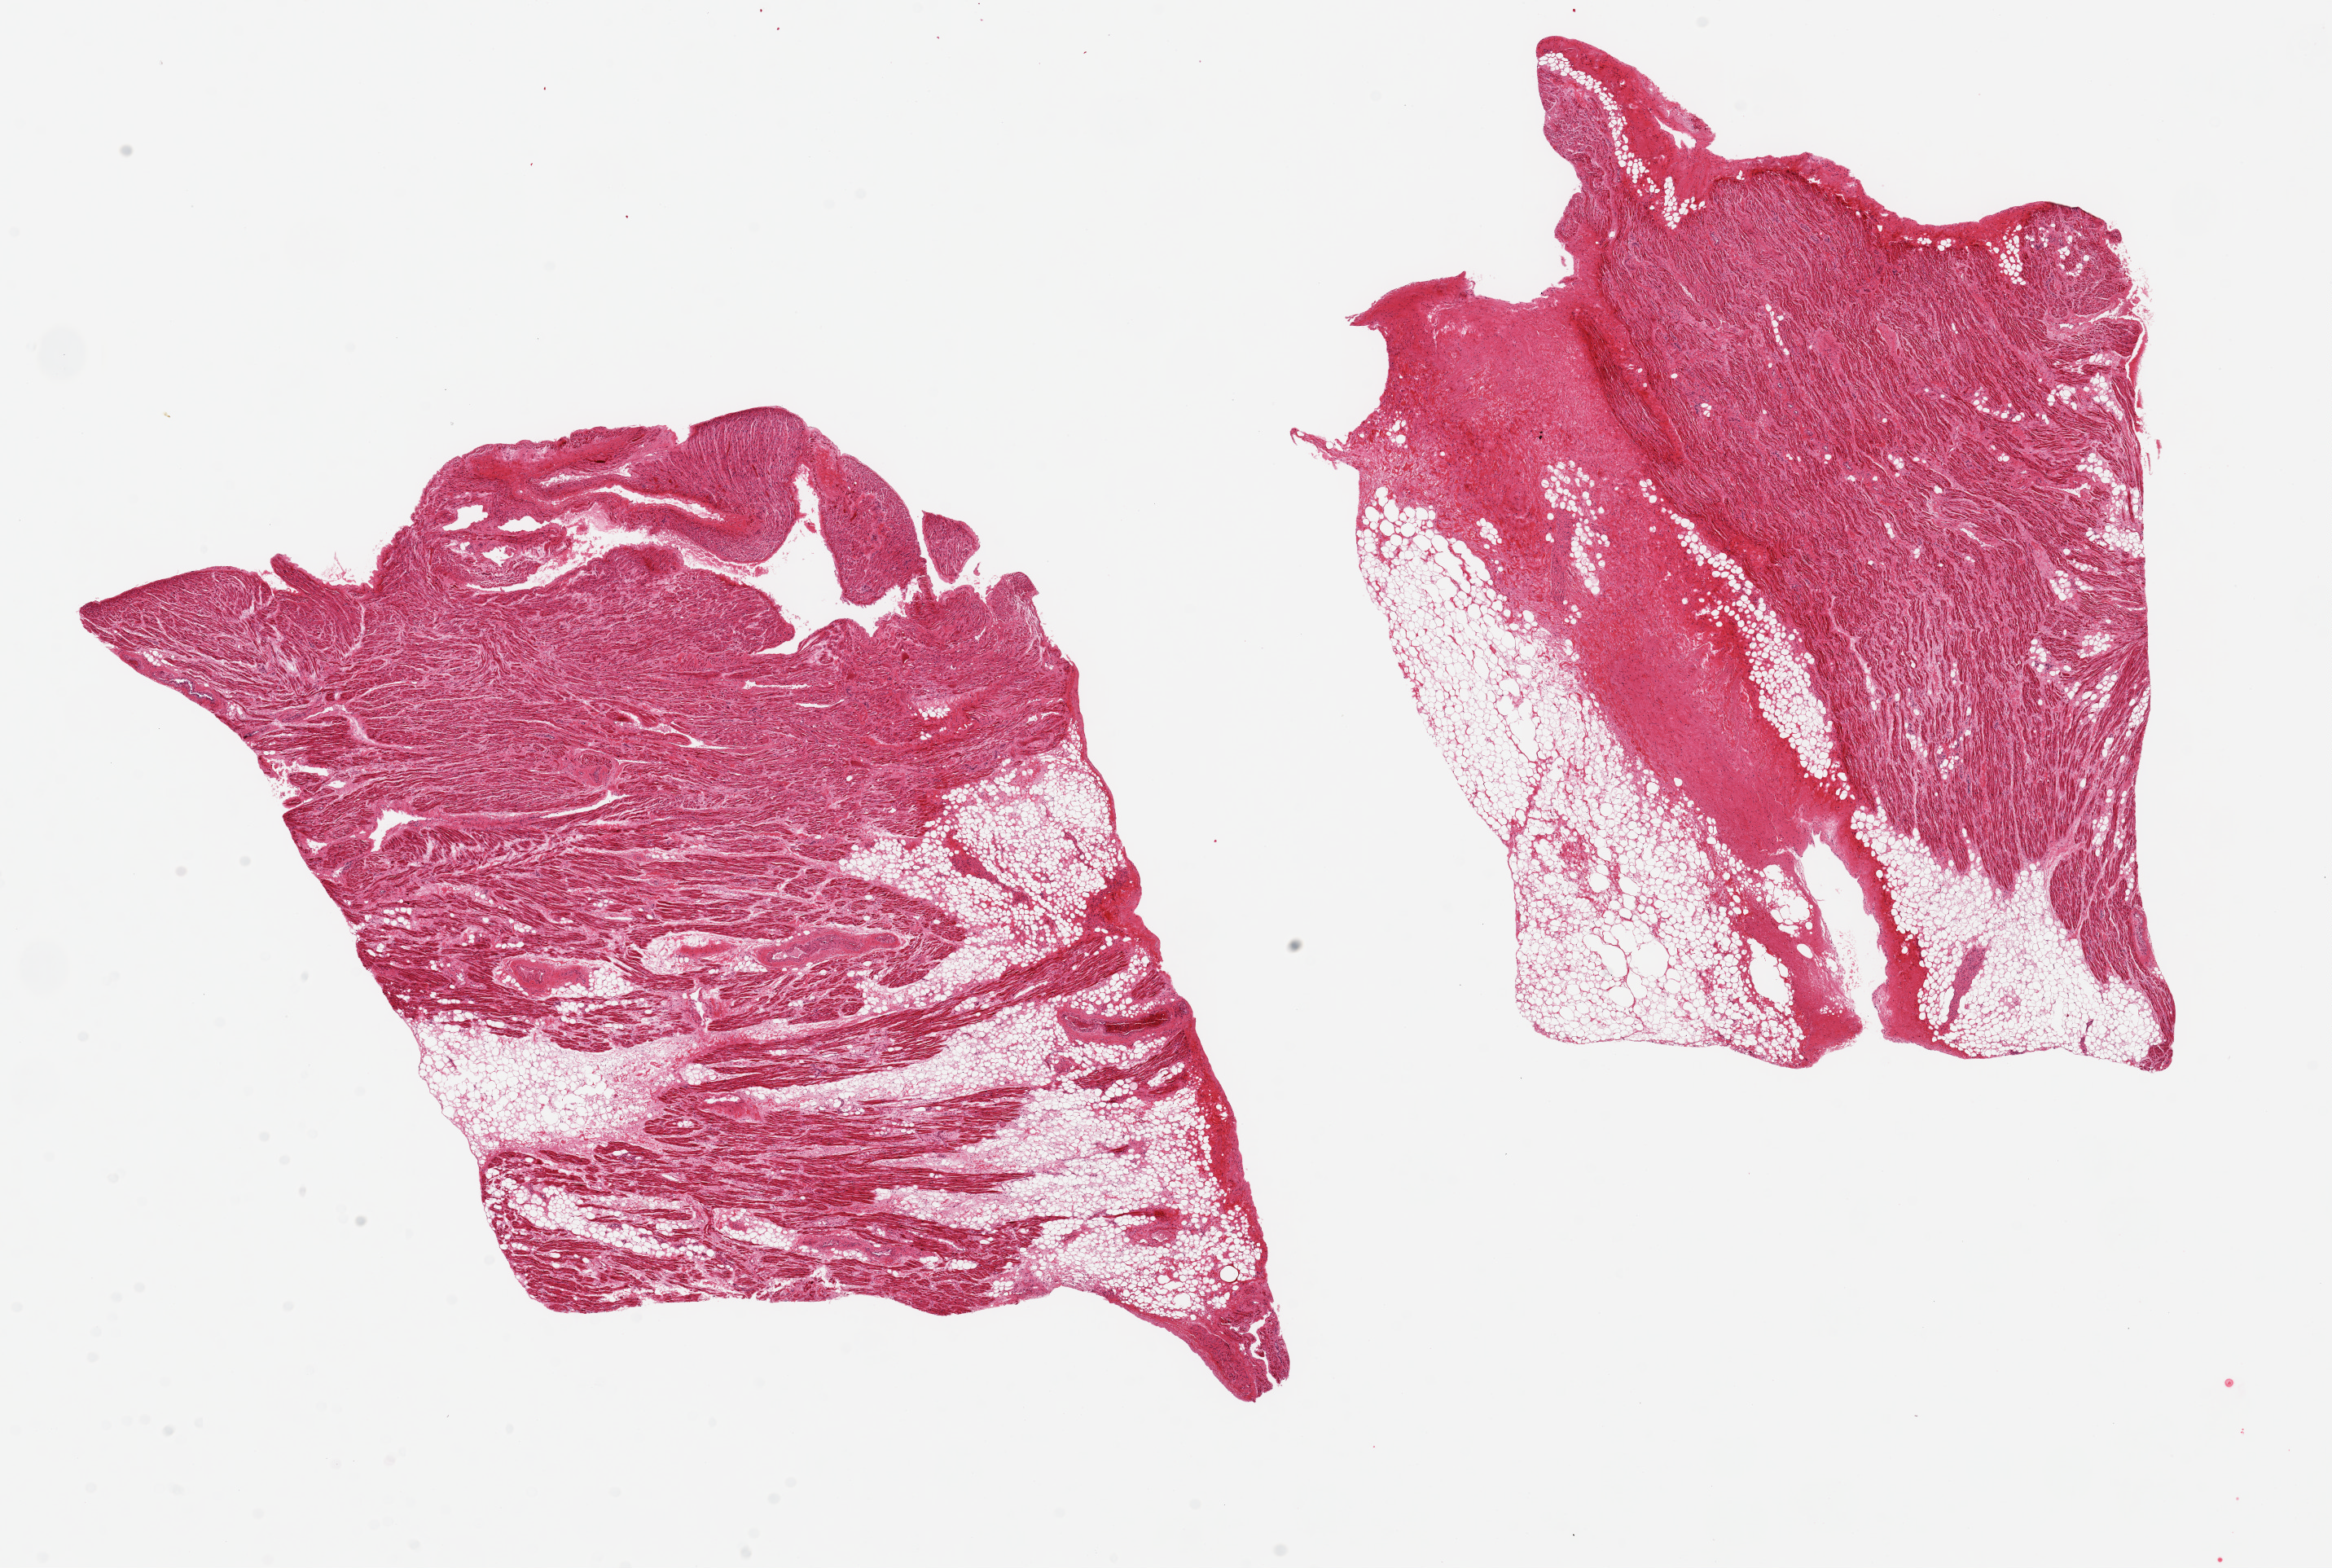
Hematoxylin and eosin (H&E) whole-slide image — shown as a low-resolution overview of the whole scanned area (about 22.6 x 15.2 mm, acquisition: 20x scan), PAXgene-fixed, paraffin-embedded tissue, section of auricular appendage (target tissue), donor tissue sample. Donor: male.
Reviewer comment on this tissue sample: 2 pieces, 11x9 & 12x8mm; ~40% external and internal fibroadipose tissue.